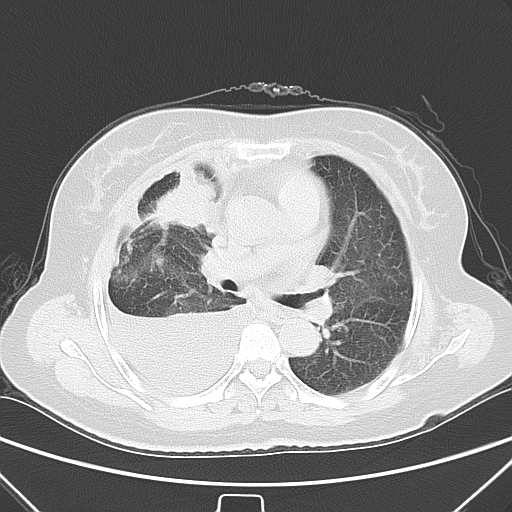
Chest CT, one axial slice. Slice 35 of 55 in the series (ordered by position). Lung window (W 1500 / L -600 HU). 5 mm slice thickness. 512 × 512 image matrix. Female patient, age 66 years. From the clinical record (not read from this slice): clinical TNM (as recorded): T2 N0 M1.
Structures marked on this image (bounding box drawn by a radiologist):
- lung tumour (recorded histology: adenocarcinoma): box from (x=148, y=168) to (x=219, y=231) px